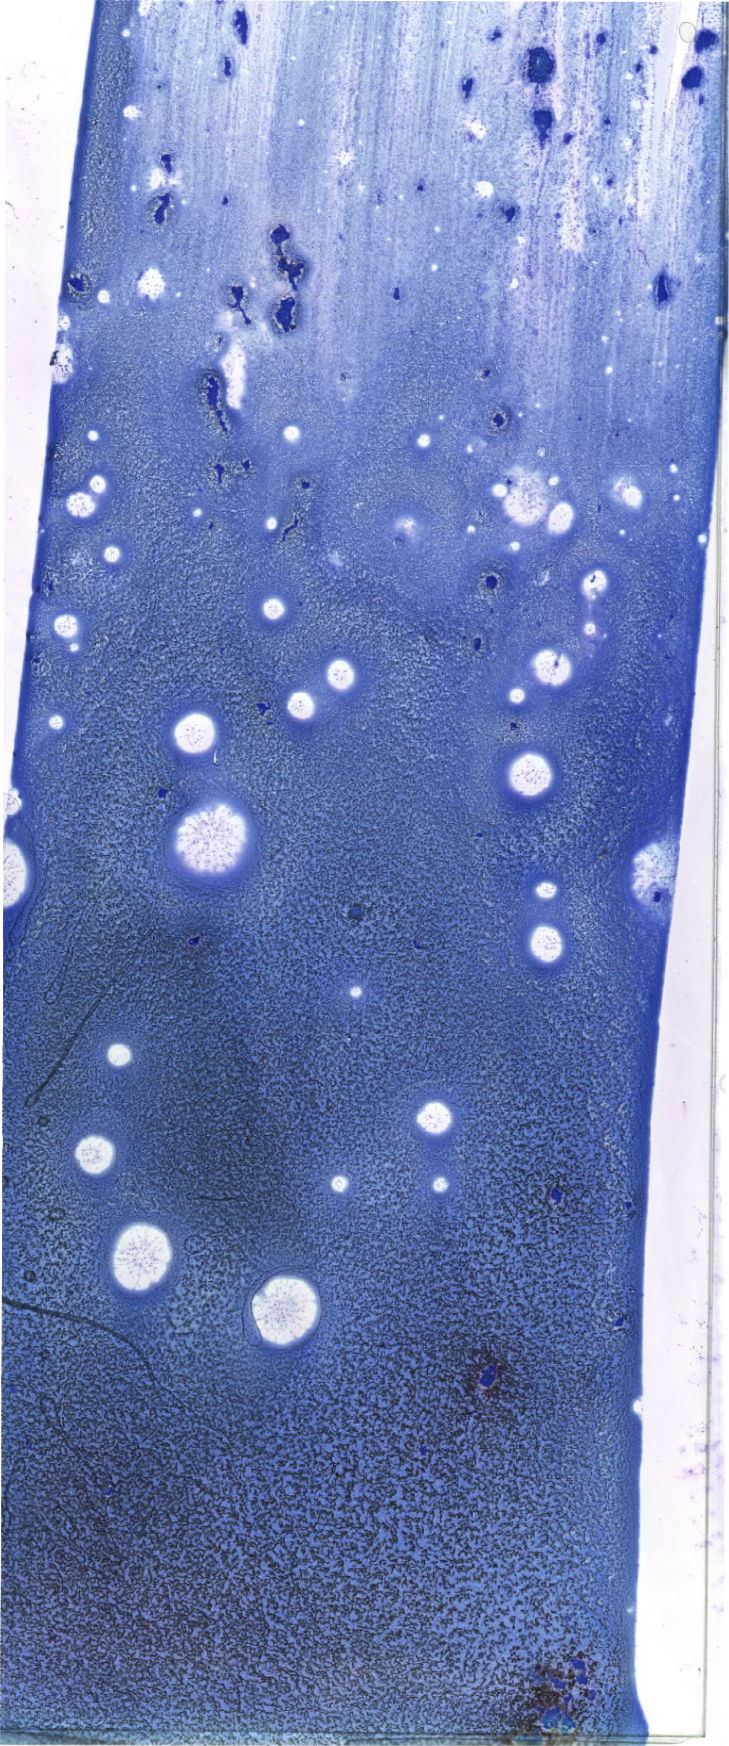
Whole-slide image of a May-Grünwald-Giemsa (MGG)-stained bone marrow aspirate smear — whole scanned area (about 20.7 x 49.5 mm) shown as a low-resolution overview.
Diagnosis: Acute Myeloid Leukemia without Maturation.